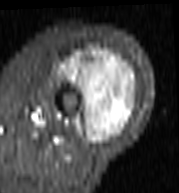
MRI of an extremity soft-tissue mass, one axial slice. Slice 48 of 103 in the series (ordered by position). STIR. MR volume resampled by the dataset authors to the PET/CT grid (not the native acquisition matrix). 3.27 mm slice thickness. 179 × 193 image matrix, field of view 175 × 188 mm. Female patient. From the clinical record (not read from this slice): histological type: undifferentiated – high grade; grade: high; site of the primary tumour: left thigh.
Structures marked on this image (expert contour drawn on MRI and transferred to this co-registered scan by the dataset authors):
- gross tumour volume including surrounding oedema: bounding box (x1, y1, x2, y2) in pixels: (52, 46, 138, 145)
- gross tumour volume (mass): (61, 51, 137, 145)